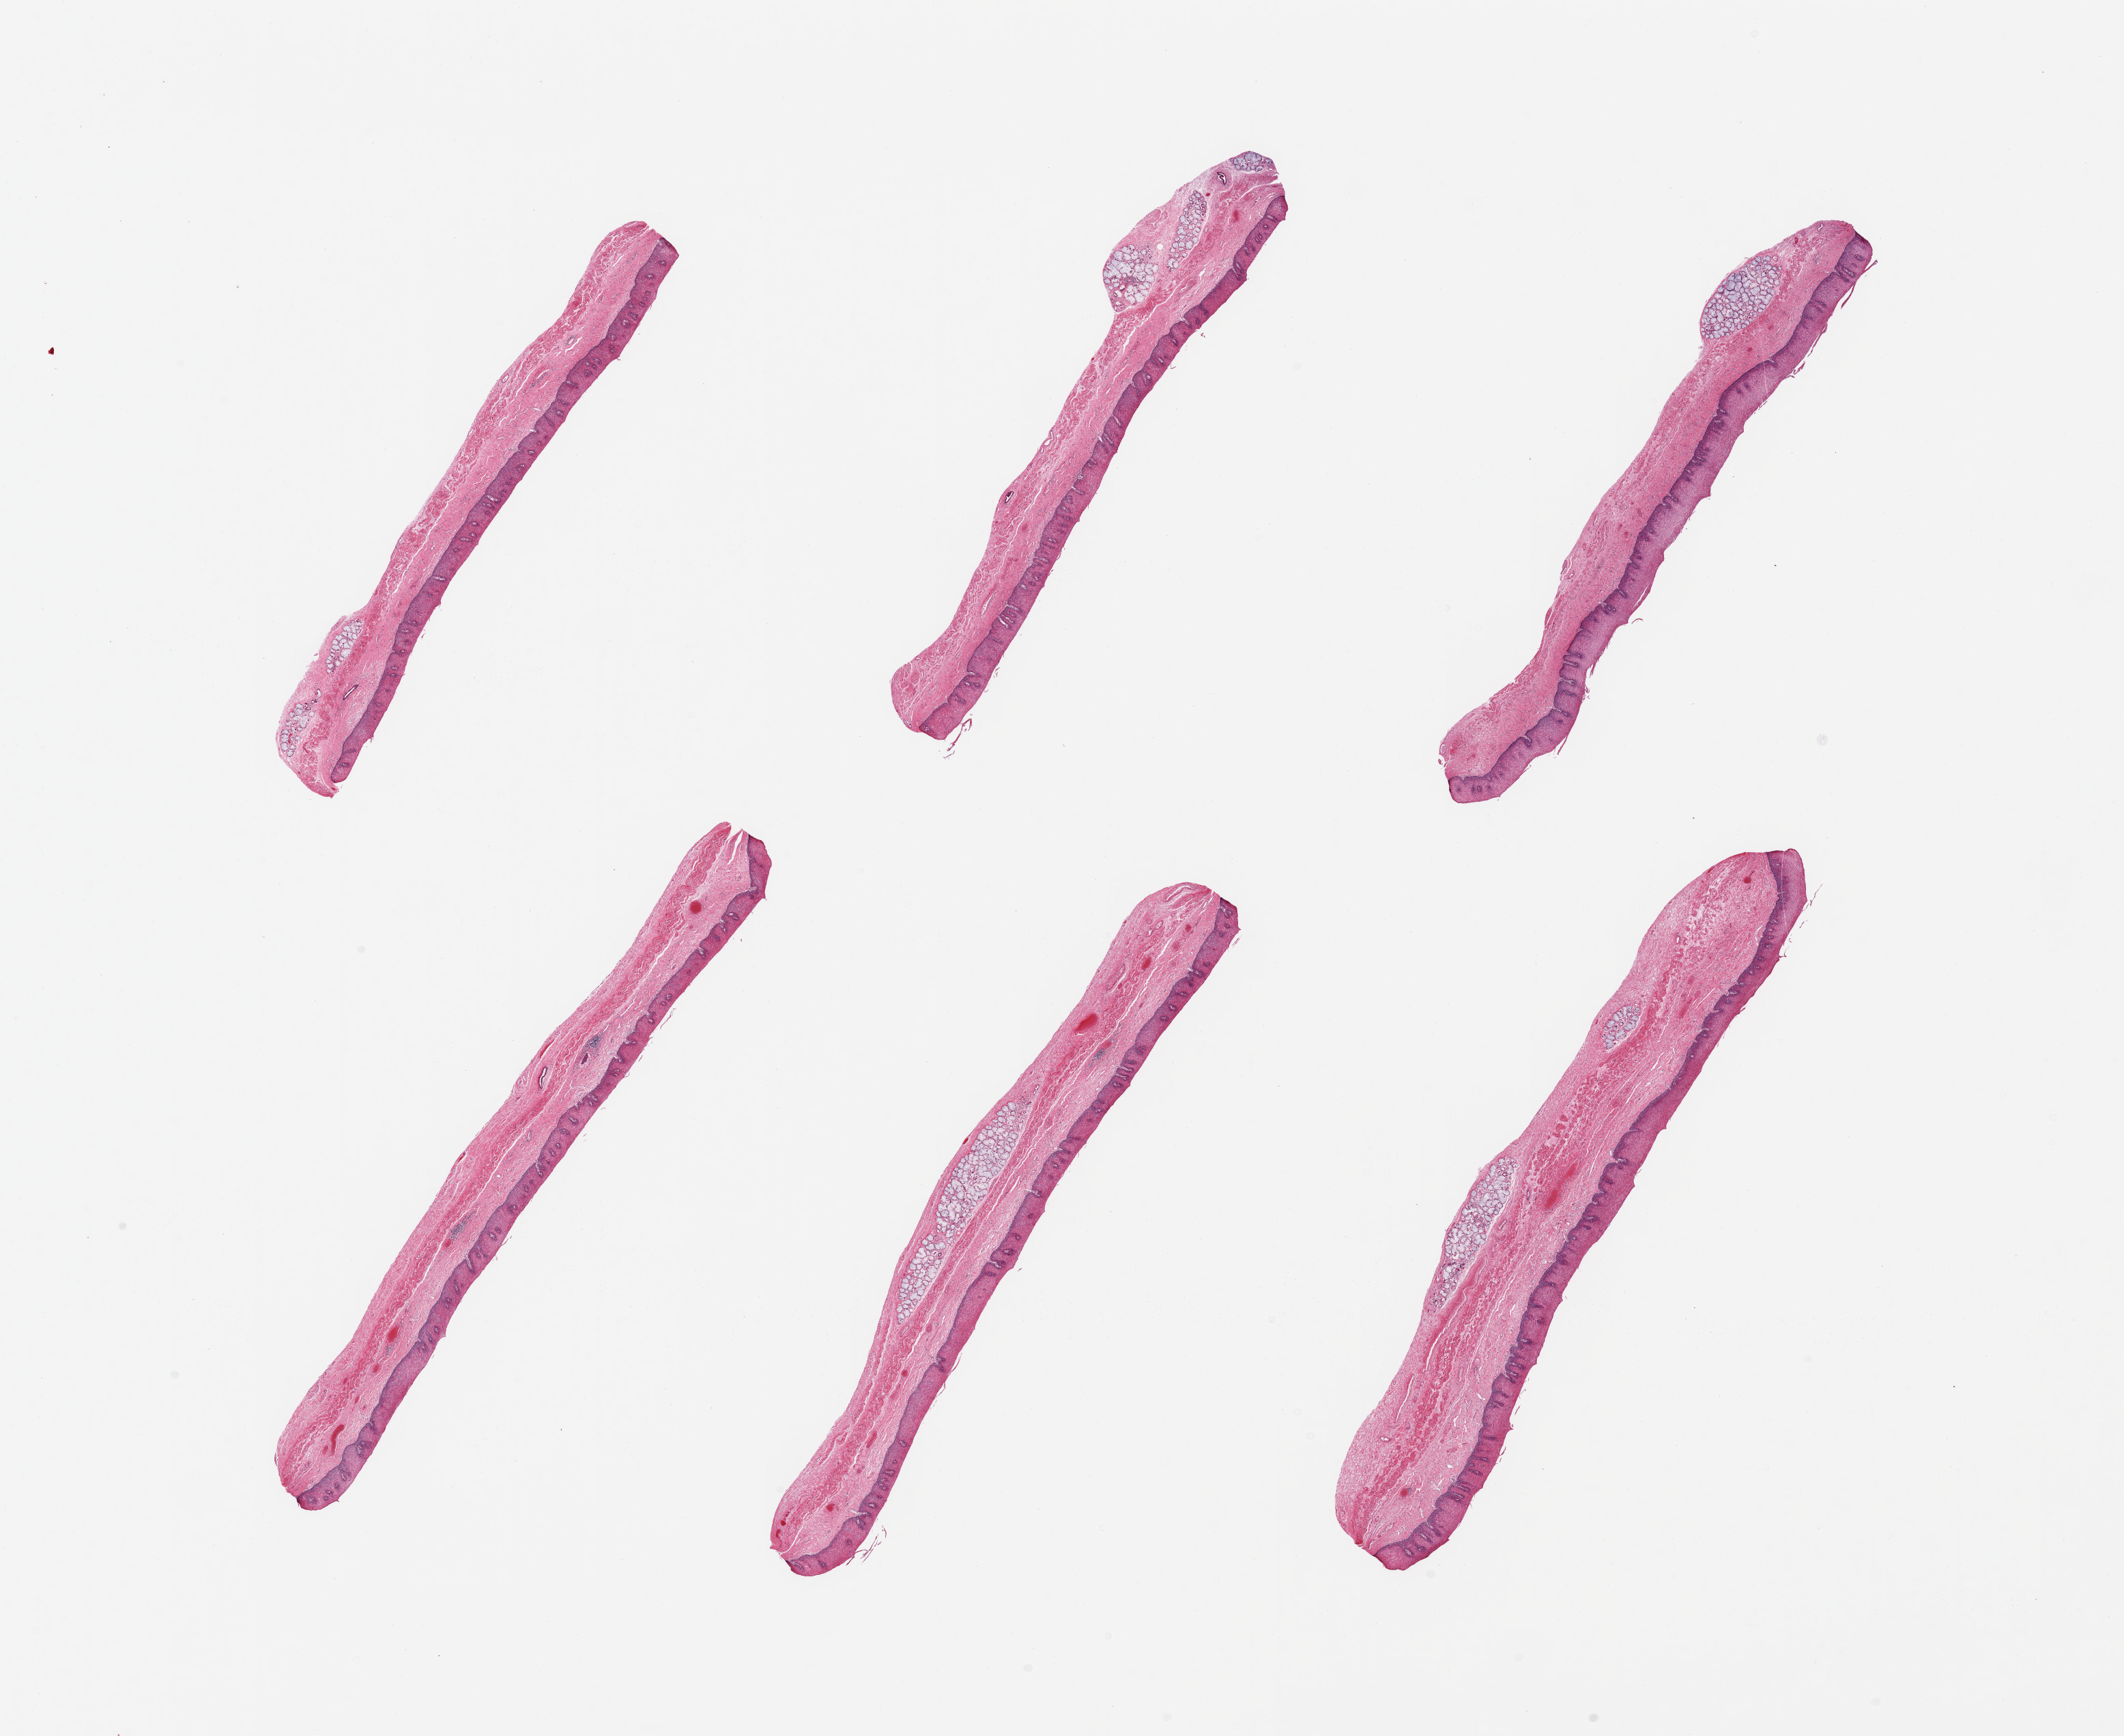
Digitized hematoxylin and eosin (H&E)-stained section, brightfield — whole scanned area (about 24.6 x 20.1 mm) shown as a low-resolution overview; PAXgene-fixed paraffin-embedded (PFPE) section; section of esophageal mucous membrane (target tissue); donor tissue sample.
Reviewer comment on this tissue sample: 6 pieces; ~ 280 microns stratified squamous epithelium; submucosal glands.